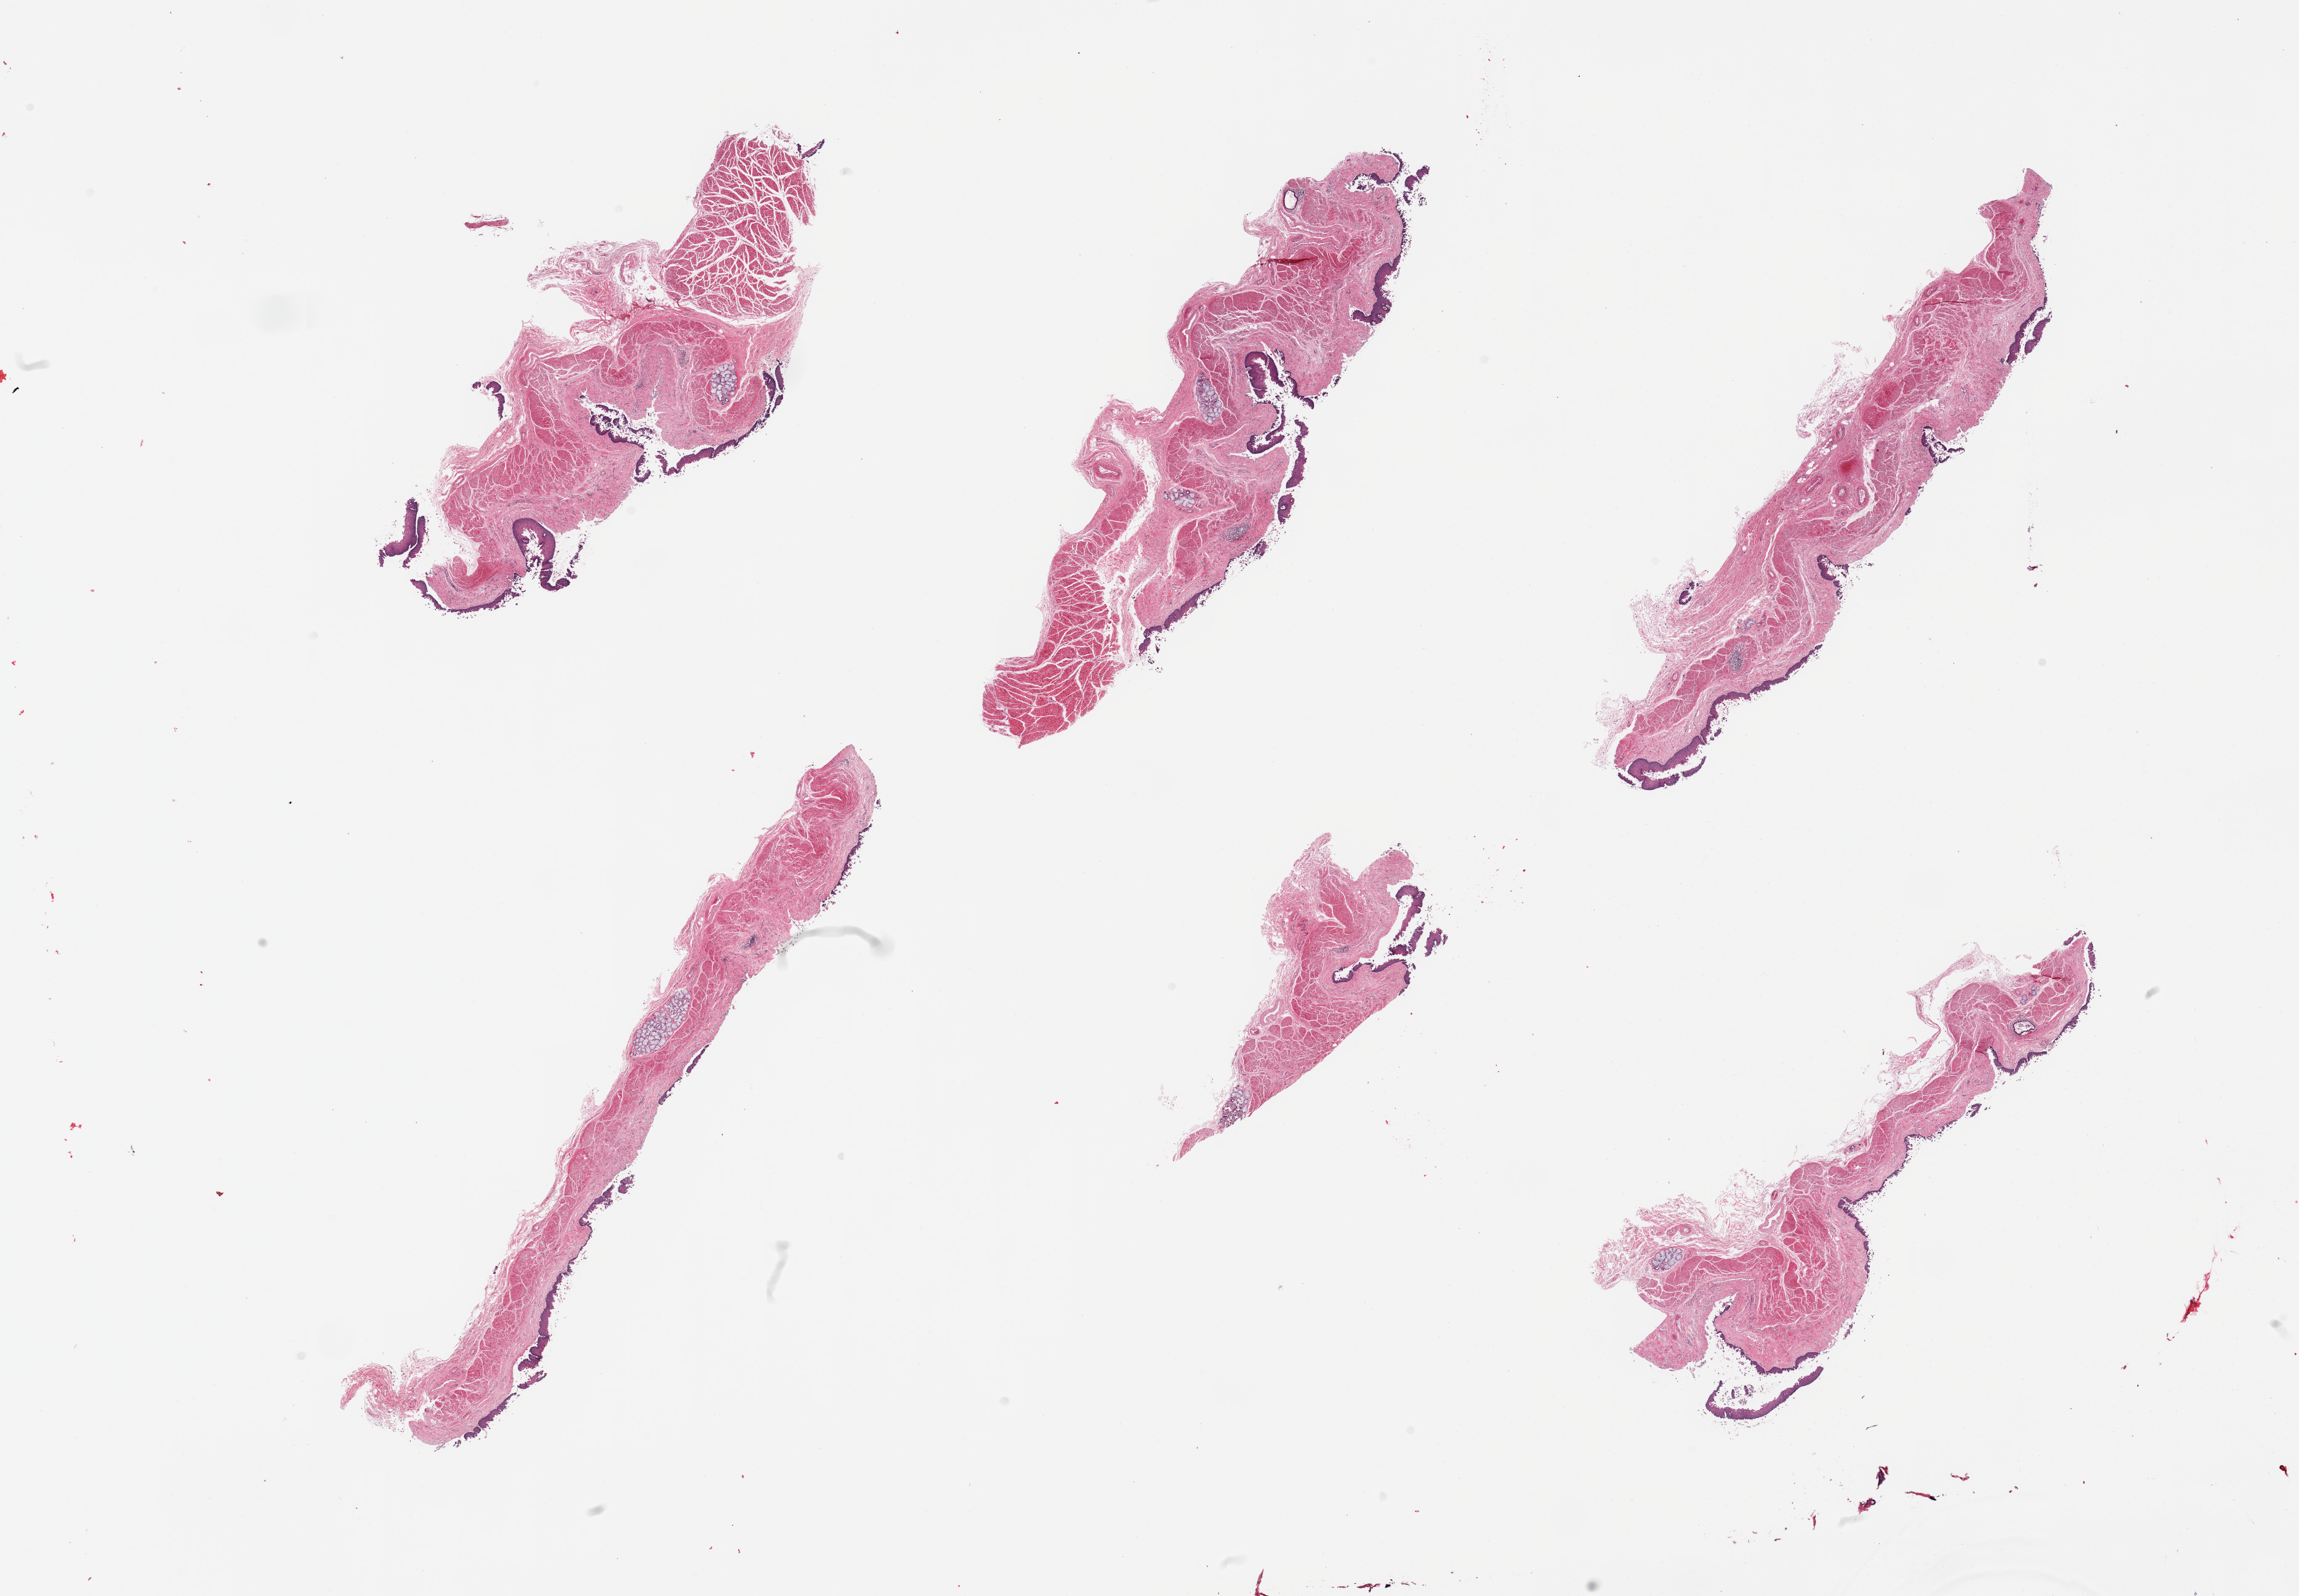
Digitized hematoxylin and eosin (H&E)-stained section — low-resolution overview of the scanned area, about 29.5 x 20.5 mm (slide scanned at 20x). PAXgene-fixed, paraffin-embedded tissue. Target tissue: esophageal mucous membrane. Donor tissue sample. Donor: male.
Review note (as recorded): 6 pieces; epithelium largely sloughed; muscularis propria [not target] sampled on 2 of 6.